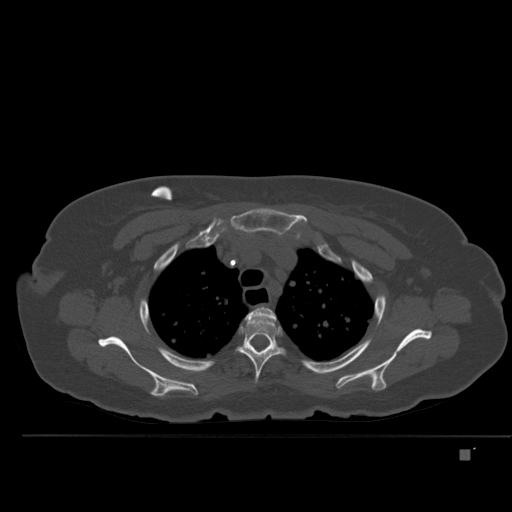
CT including the spine, one axial slice. Slice 380 of 477 in the series (ordered by position). Bone window (W 1800 / L 400 HU). 1.5 mm slice thickness. 512 × 512 image matrix, field of view 422 × 422 mm. Female patient, age 74 years. From the clinical record (not read from this slice): primary cancer: colon.
Structures marked on this image (semi-automatically segmented with operator editing):
- T2 vertebra: bounding box (x1, y1, x2, y2) in pixels: (248, 306, 277, 320)
- T3 vertebra: (237, 313, 285, 384)